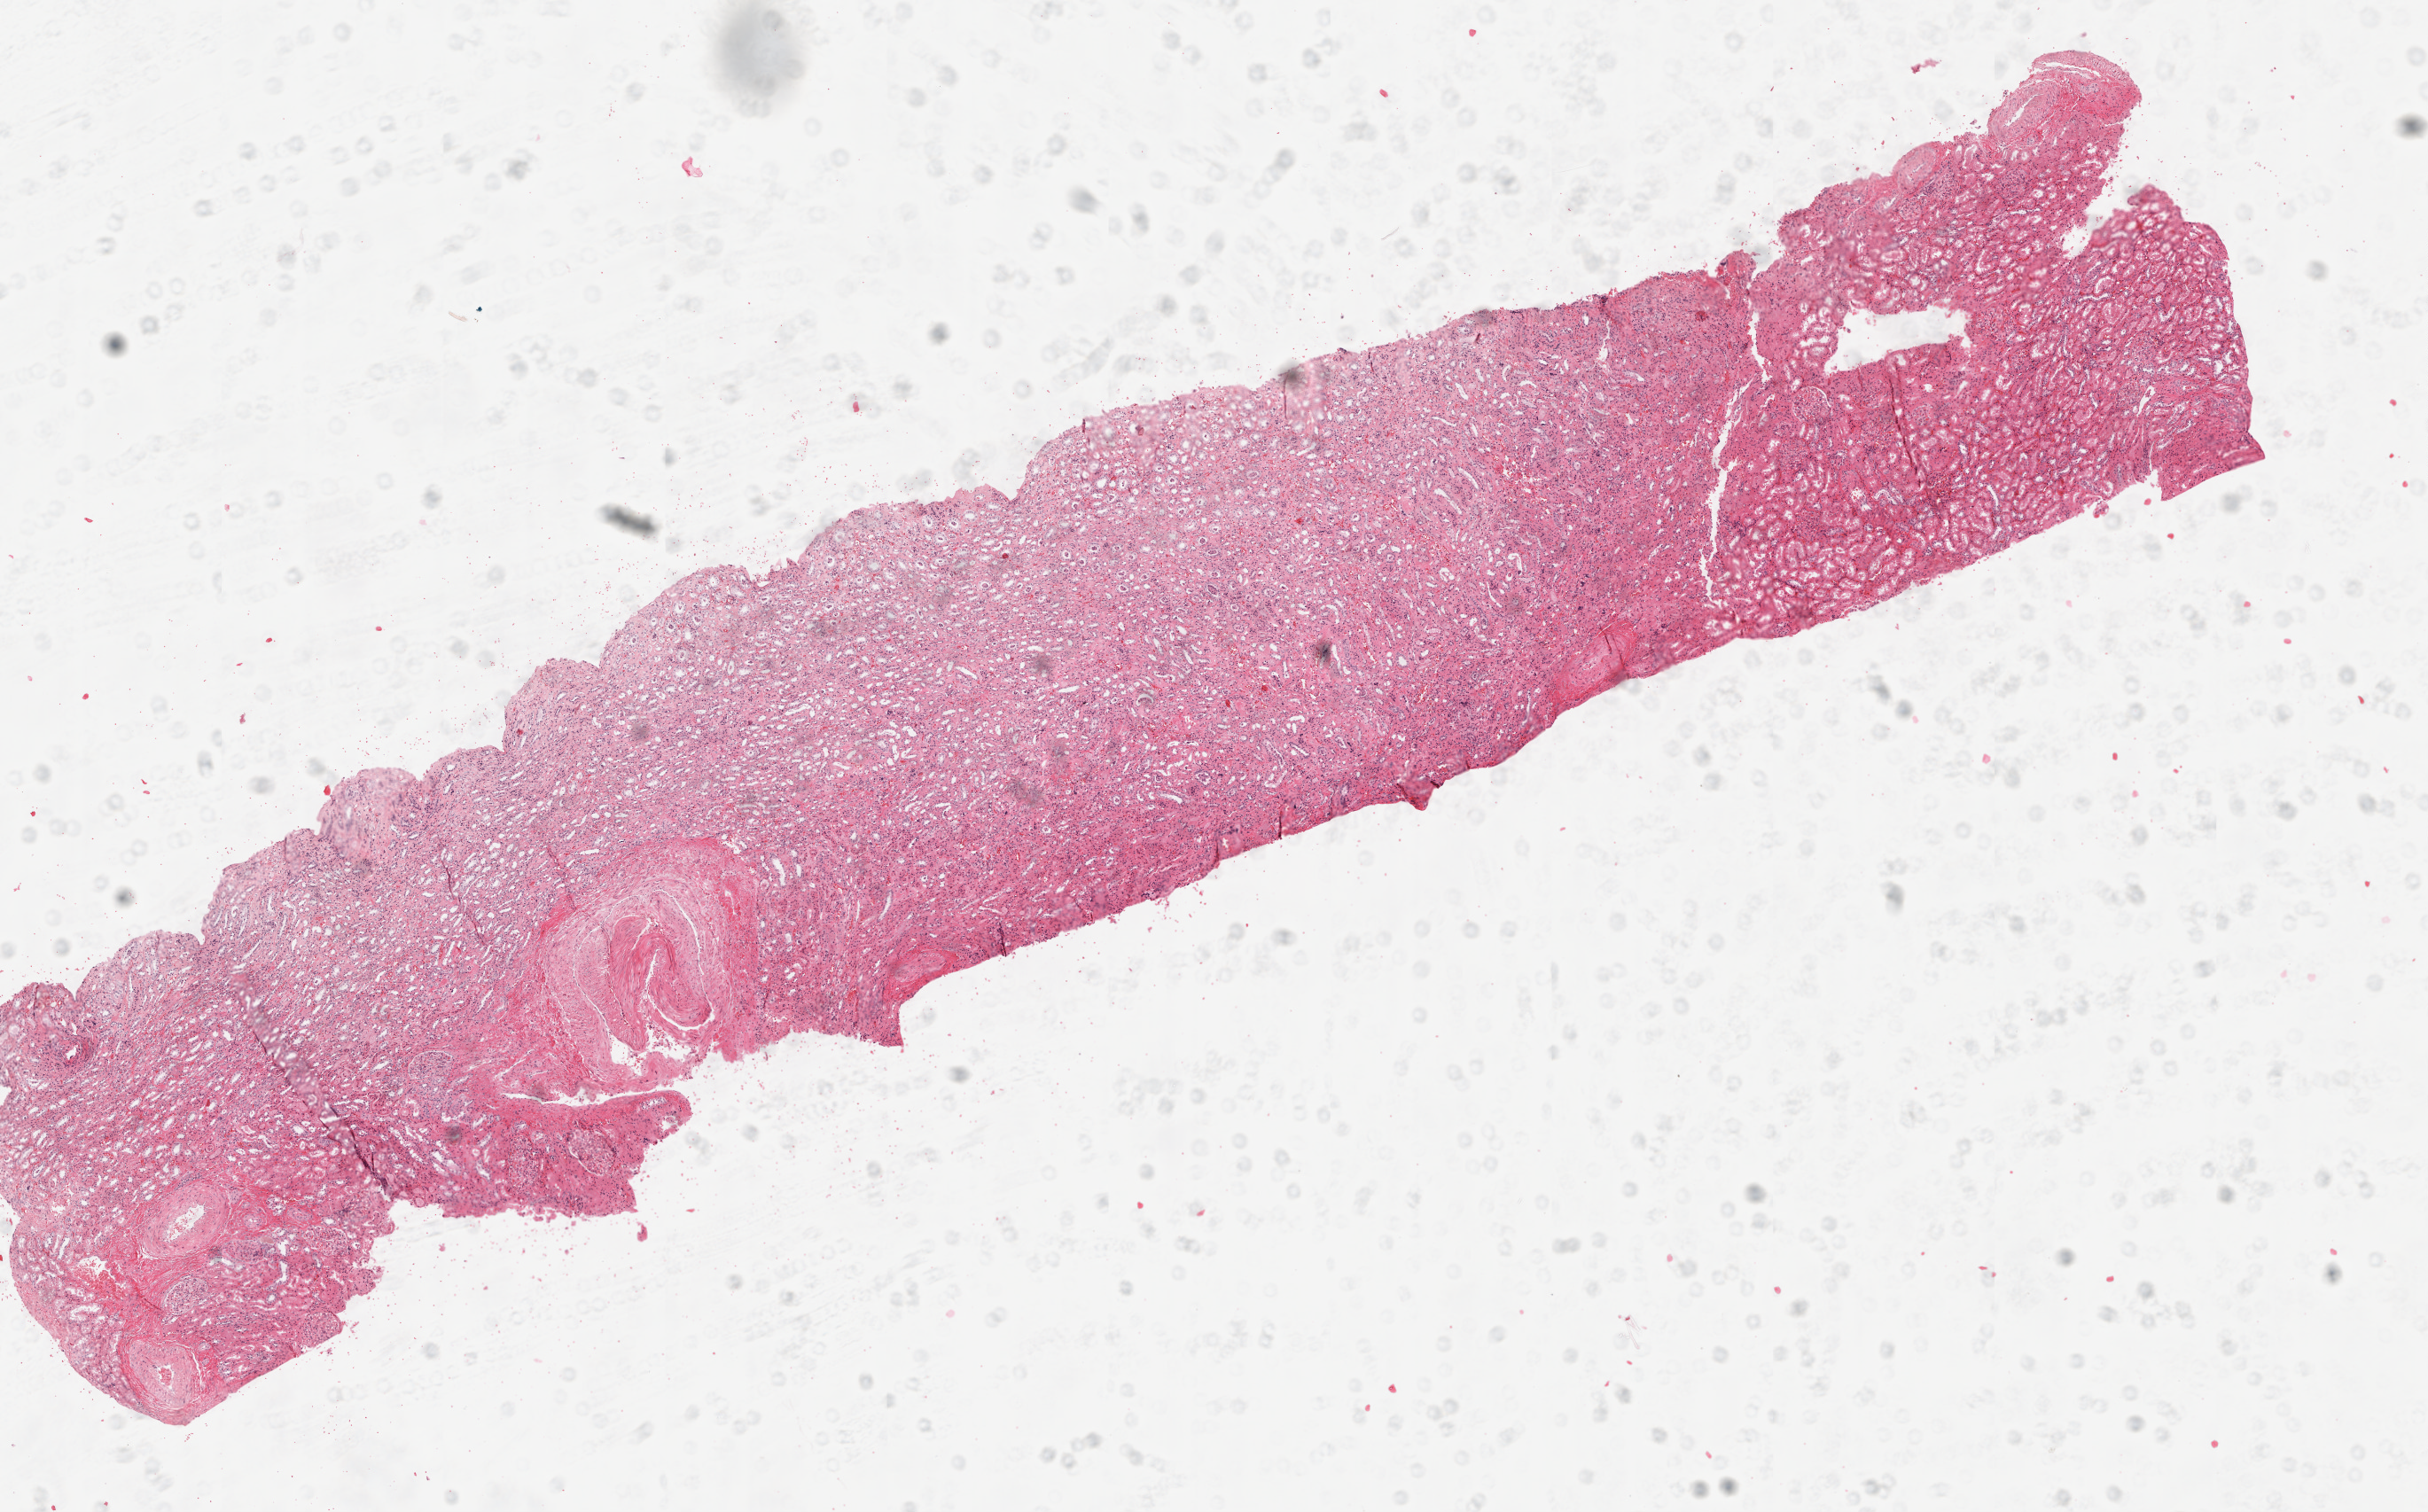
Digitized Hematoxylin and eosin (H&E) stained tissue section (whole slide) — shown as a low-resolution overview of the whole scanned area (about 10.9 x 6.8 mm); kidney, normal (non-tumour) tissue. 41-year-old male patient.
This section: normal (non-tumour) tissue from the same patient. Patient diagnosis: Renal cell carcinoma, NOS.